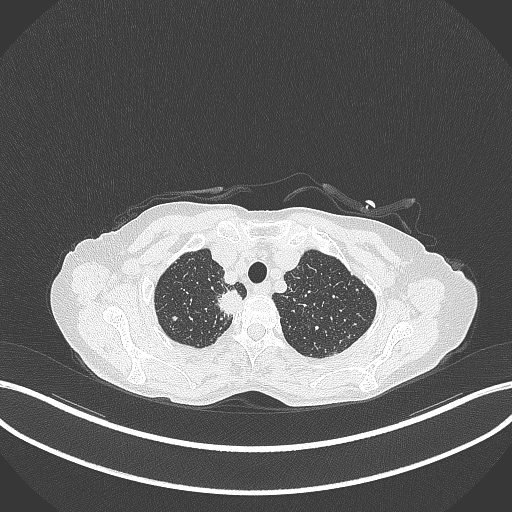
Chest CT, one axial slice; position 322 of 403 along the scan axis; lung window (W 1500 / L -600 HU); 512 × 512 image matrix, field of view 400 × 400 mm. Patient: female, 75 years. From the clinical record (not read from this slice): clinical TNM (as recorded): T1c N1 M1.
Annotated regions visible in this slice (bounding box drawn by a radiologist):
- lung tumour (recorded histology: adenocarcinoma): bounding box [x1, y1, x2, y2] px = [212, 289, 247, 320]